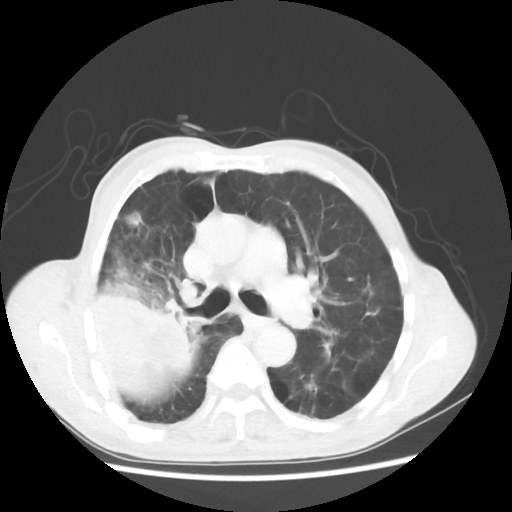
Chest CT, one axial slice. Position 33 of 58 along the scan axis. Reconstruction kernel STANDARD. 100 kVp. Lung window (W 1500 / L -600 HU). 5 mm slice thickness. 512 × 512 image matrix, field of view 351 × 351 mm. Patient: male, 75 years. From the clinical record (not read from this slice): clinical TNM (as recorded): T4 N1 M1.
Outlined on this slice (rectangle marked by the reading radiologist):
- lung tumour (recorded histology: adenocarcinoma): bounding box <93,278,205,406> (left, top, right, bottom; pixels)